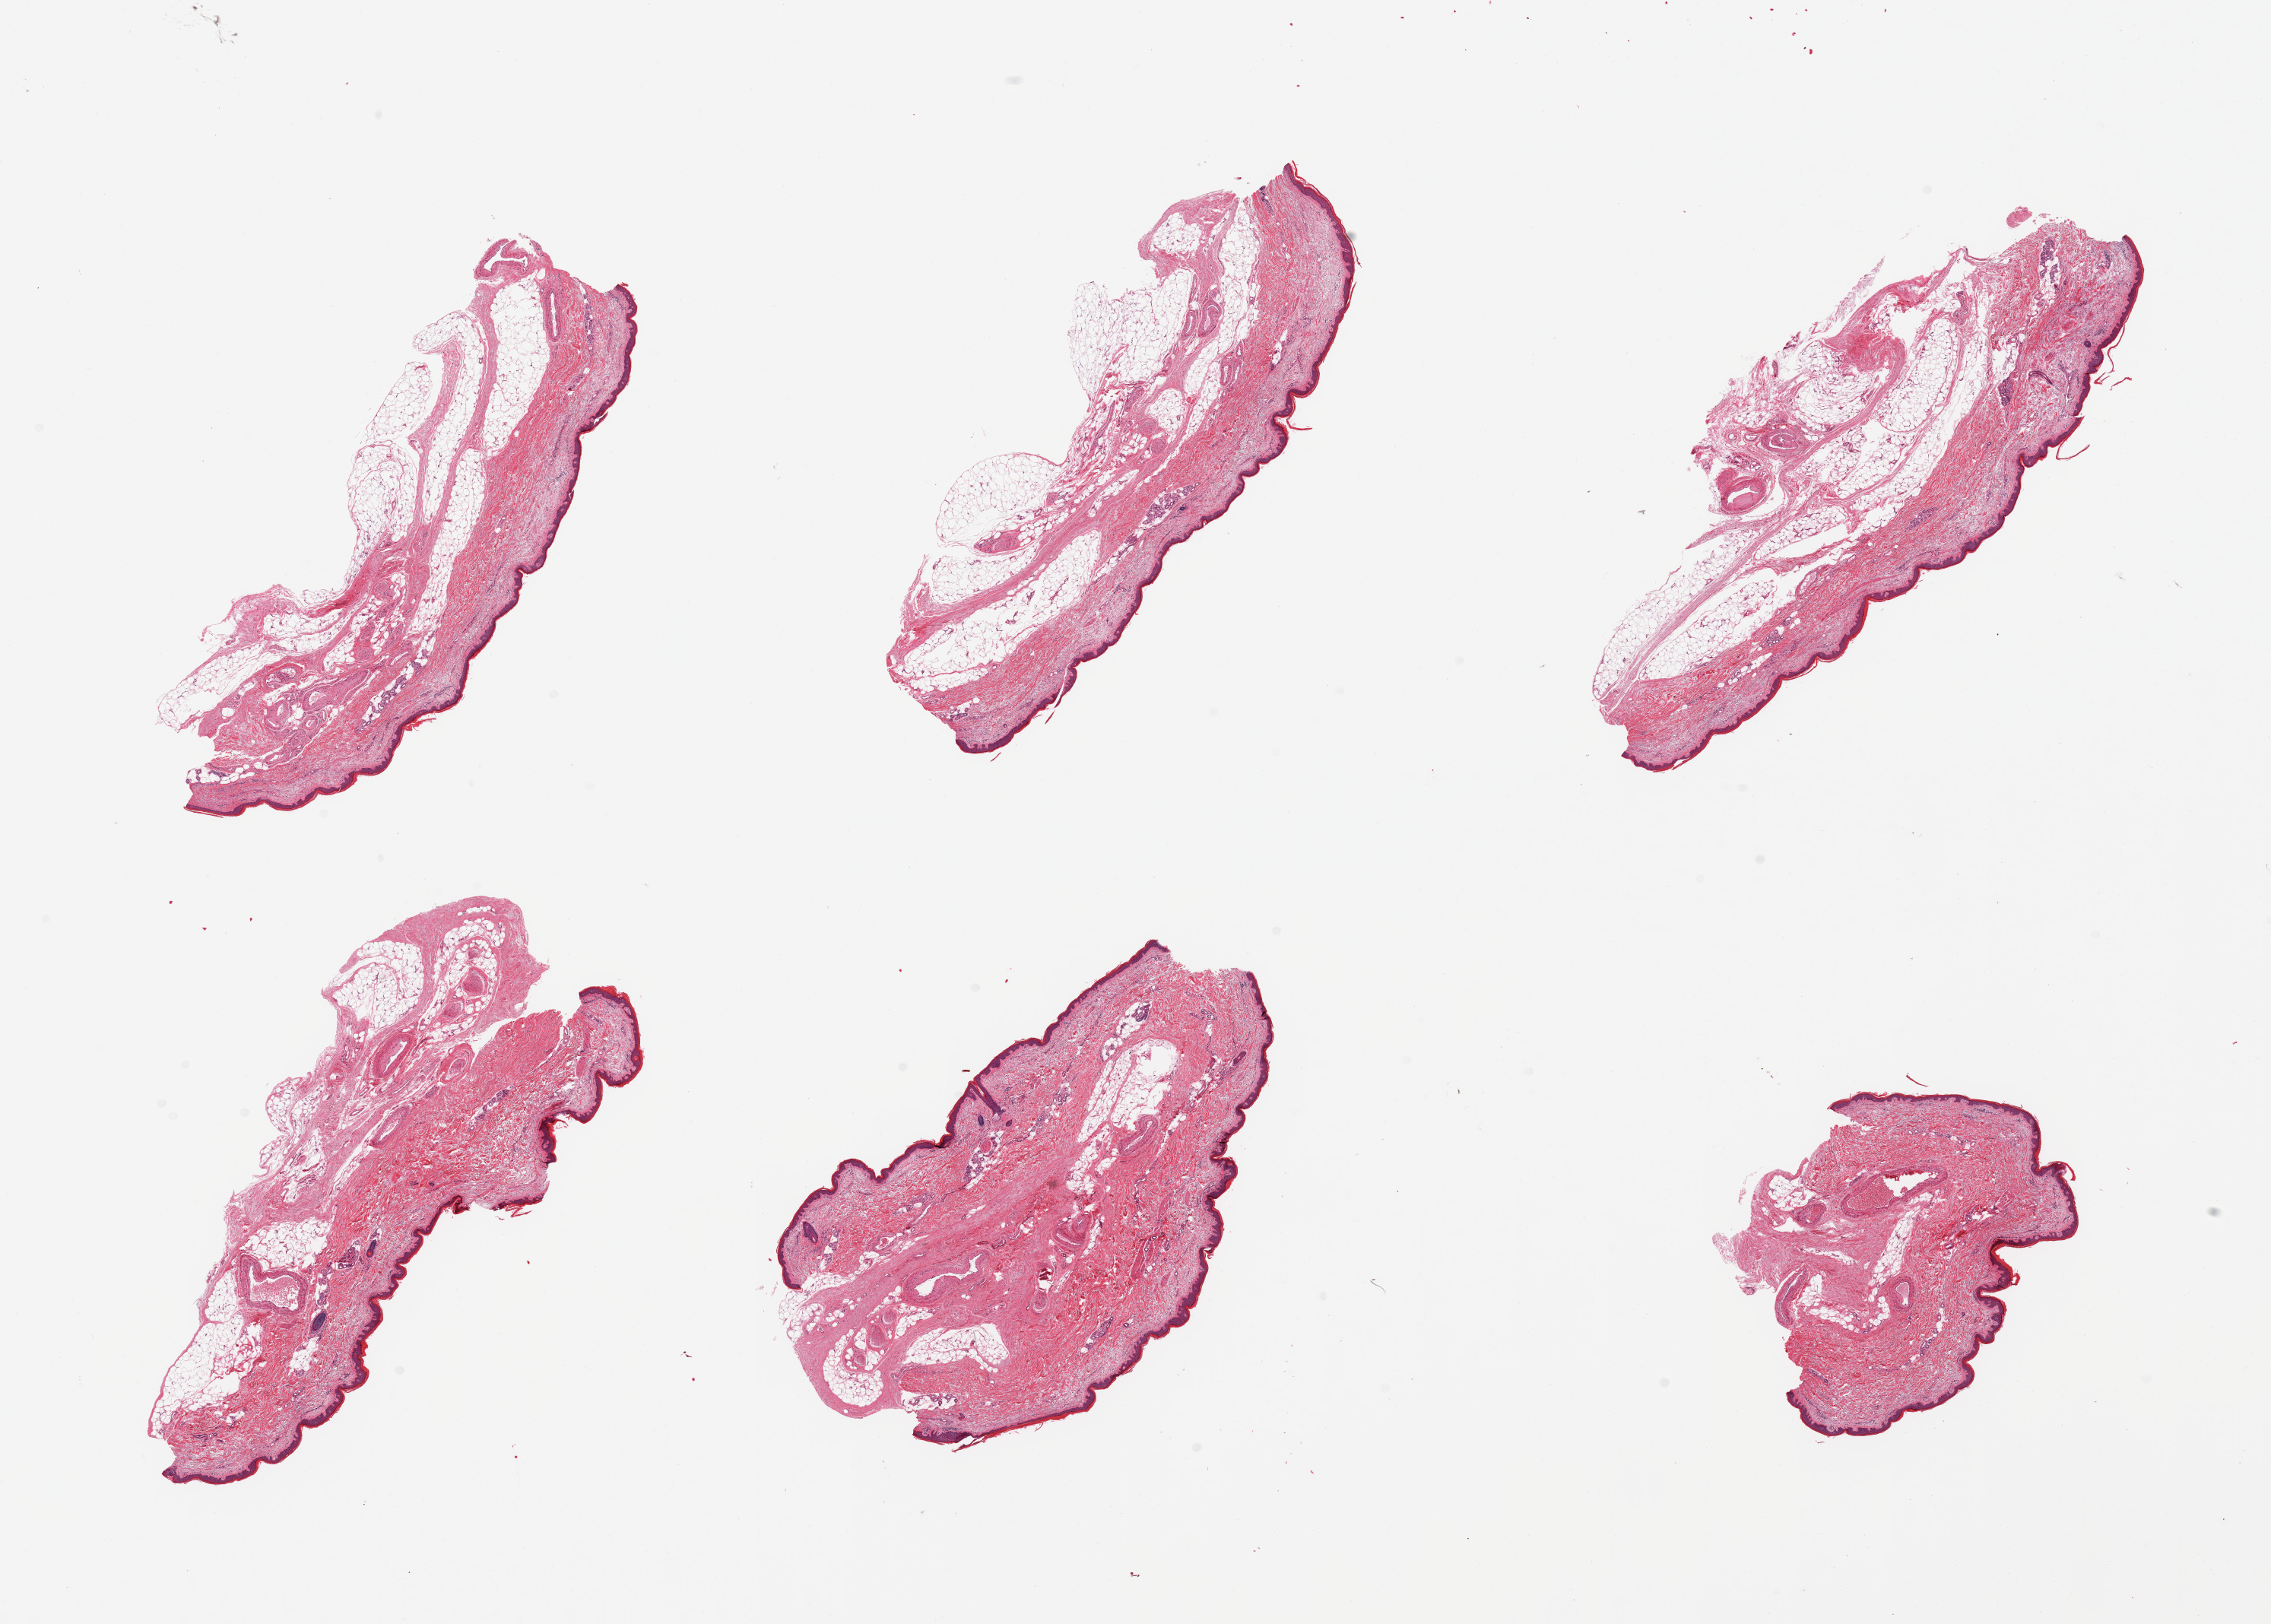
Whole-slide image, haematoxylin and eosin stain — shown as a low-resolution overview of the whole scanned area (about 23.6 x 16.9 mm, acquisition: 20x scan); PAXgene-fixed paraffin-embedded (PFPE) section; sampled site (target tissue): skin of lower leg; tissue donor sample. Male donor.
- review note (as recorded): 6 pieces, adherent dermal fat up to ~1mm nubbins; squamous epithelium is ~50 microns